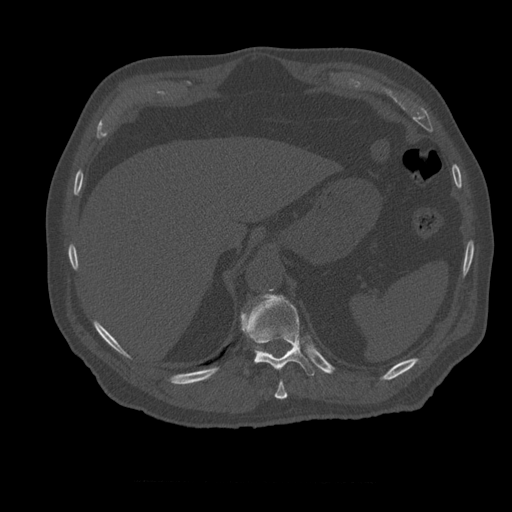
CT including the spine, one axial slice. Position 282 of 399 along the scan axis. Reconstruction kernel STANDARD. 120 kVp. Bone window (W 1800 / L 400 HU). 1.25 mm slice thickness. 512 × 512 image matrix. Patient age 73 years. From the clinical record (not read from this slice): primary cancer: prostate.
Structures marked on this image (semi-automatic segmentation, software-assisted and operator-edited):
- T10 vertebra: bounding box <275,381,288,400> (left, top, right, bottom; pixels)
- T11 vertebra: <242,294,315,376>
- T12 vertebra: <242,308,258,352>